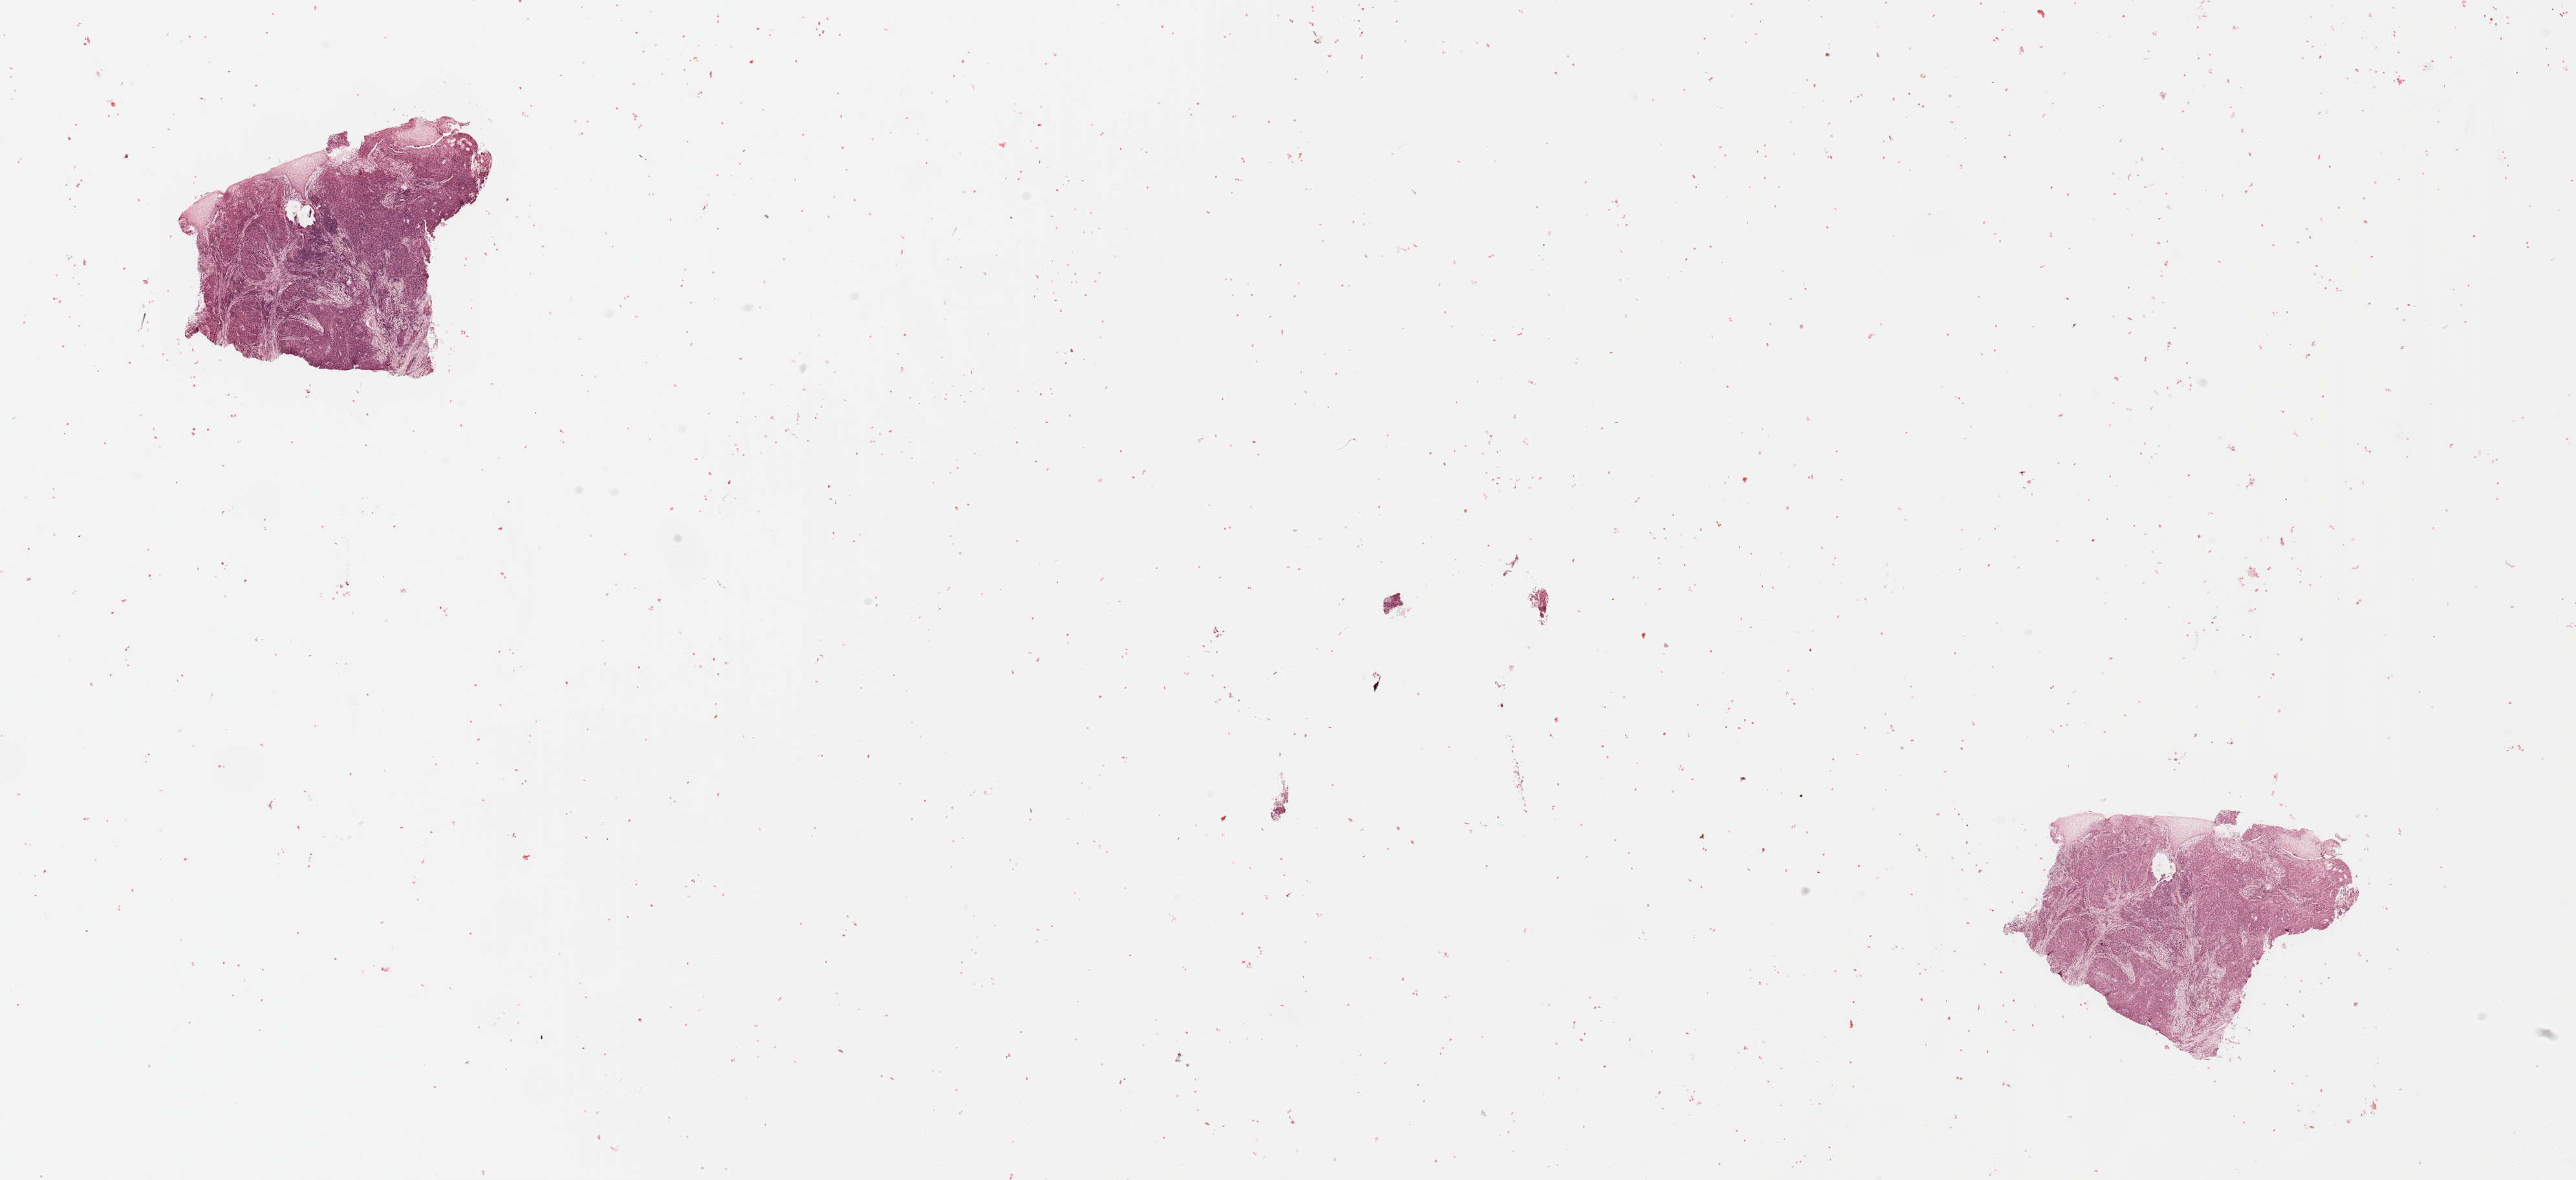
Digitized H&E tissue section (whole slide), whole scanned area (about 31.5 x 14.4 mm) shown as a low-resolution overview; tumour tissue sample, sampled site: larynx. 68-year-old male patient. Histologic grade: G2 (moderately differentiated). Slide review estimates, as recorded: tumour nuclei 80%, necrosis 3%.
Primary tumour site (as recorded): larynx. Histologic diagnosis: Squamous cell carcinoma, NOS (larynx, NOS). AJCC pathologic stage: III.